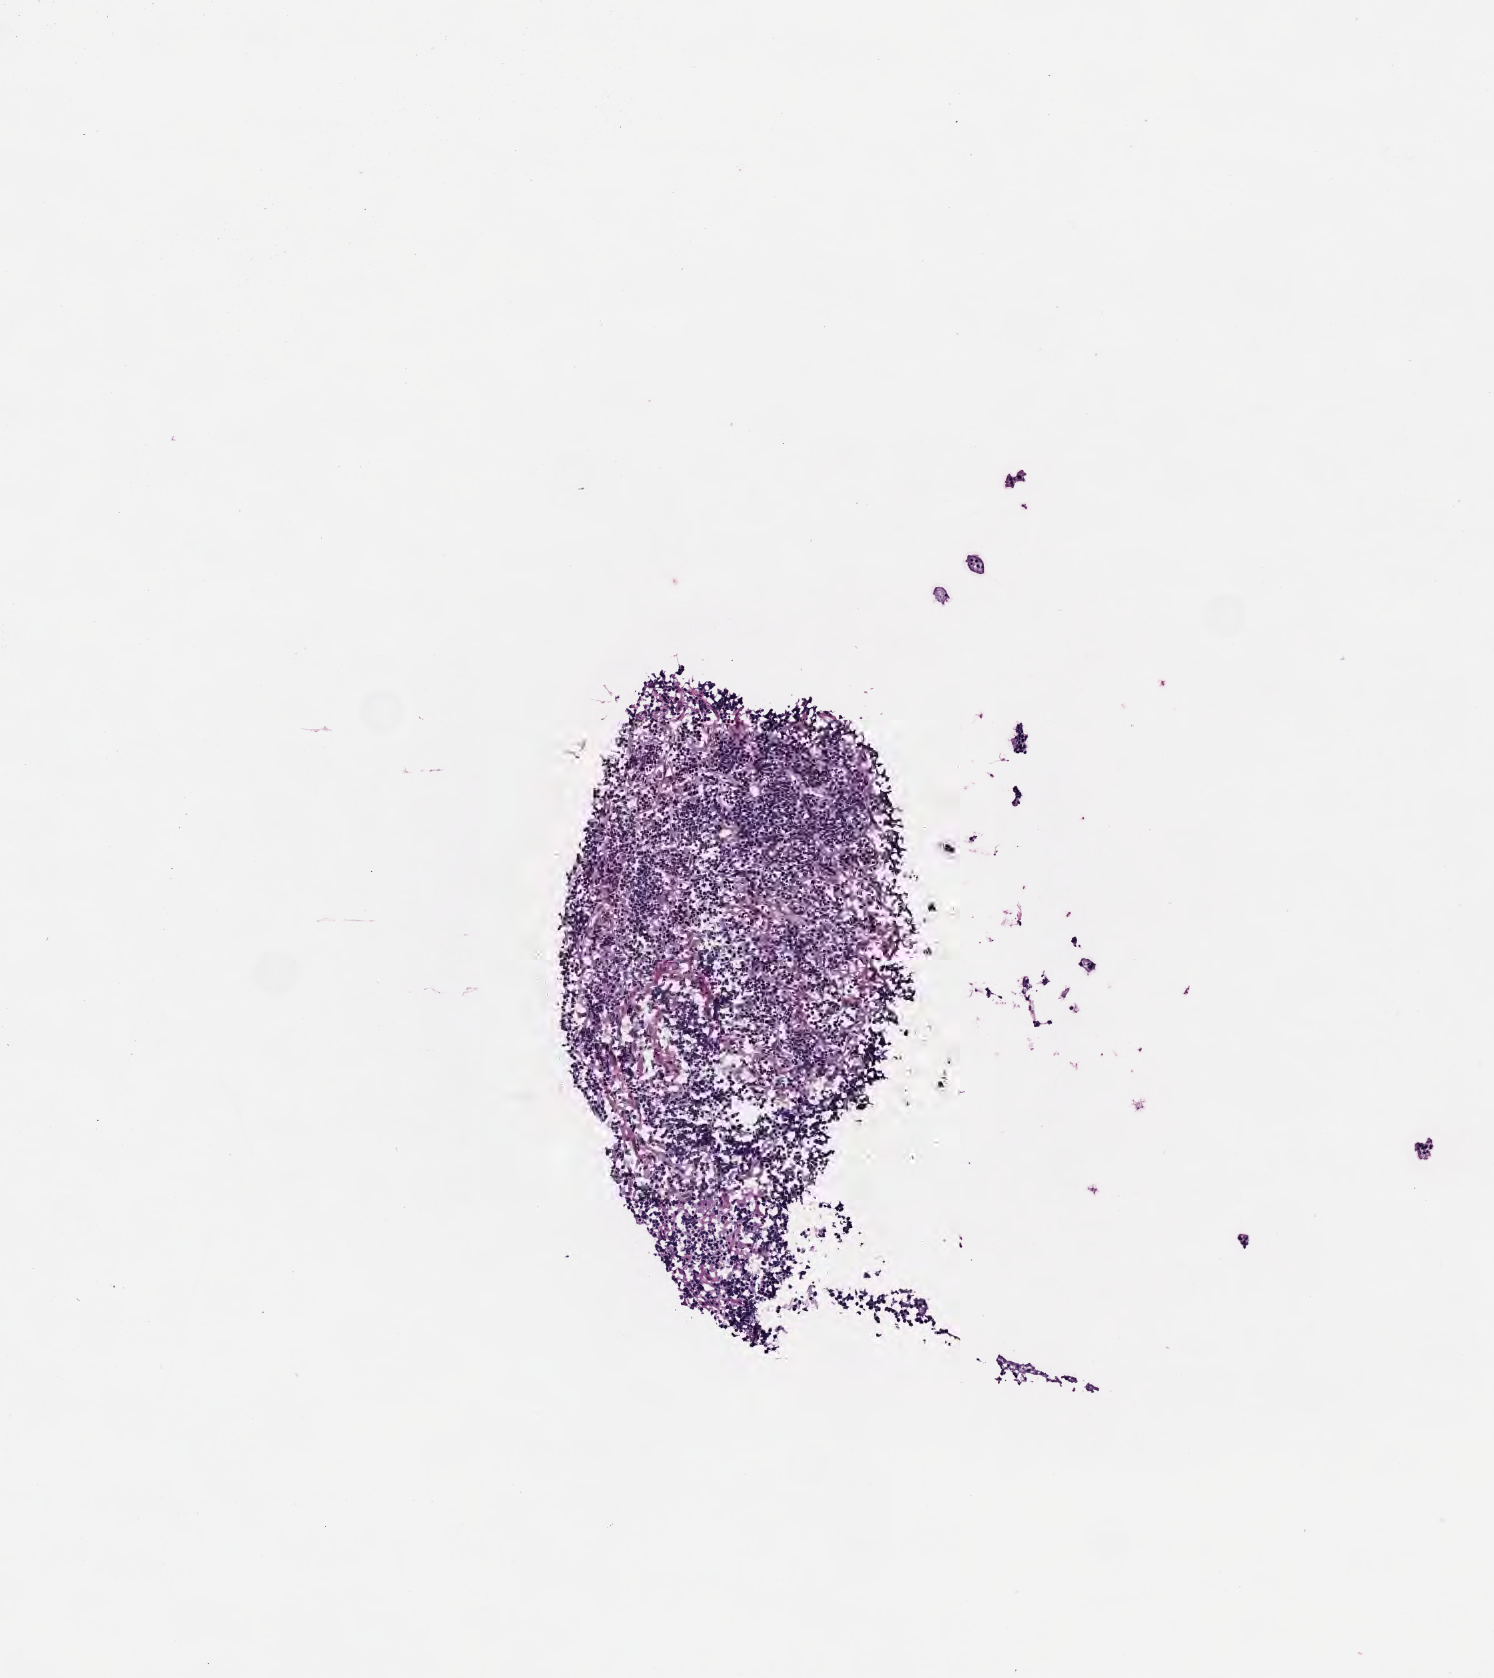
Whole-slide image, haematoxylin and eosin stain, low-resolution overview of the scanned area, about 3.0 x 3.4 mm; cryosection; primary tumor; site: ovary. Patient: female, 10 years old. Pathologist review of this section (percent, as recorded): tumor cells 95%, tumor nuclei 95%, stromal cells 5%, necrosis 0%, normal cells 0%. Infiltration values recorded for this section: lymphocyte infiltration 10%, monocyte infiltration 30%, neutrophil infiltration 10%.
- Ann Arbor stage (patient): Stage III
- histologic diagnosis: Burkitt lymphoma, NOS